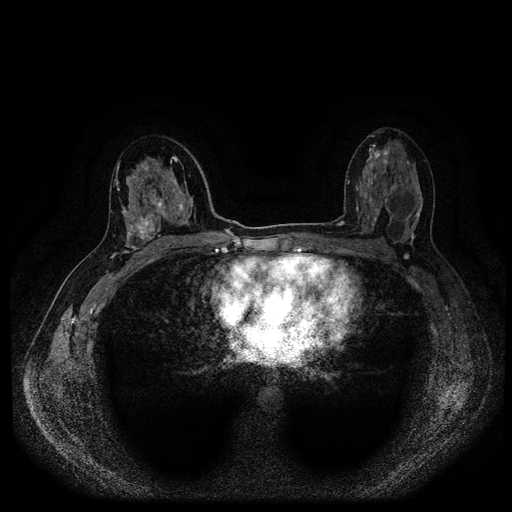
Breast MRI (dynamic contrast-enhanced, multi-phase), one axial slice. Slice 57 of 116 in the series (ordered by position). Dynamic contrast-enhanced series, time point 2 of 5 at this slice position (early post-contrast). 1.5 T. TE 2.6 ms, TR 5.4 ms. 2 mm slice thickness. 512 × 512 image matrix. Female patient, age 48 years.
Structures marked on this image (semi-automatic segmentation, software-assisted and operator-edited):
- breast lesion (labelled 'tumour' in the annotation; benign lesions carry a separate 'benign' label): bounding box <132,210,163,247> (left, top, right, bottom; pixels)